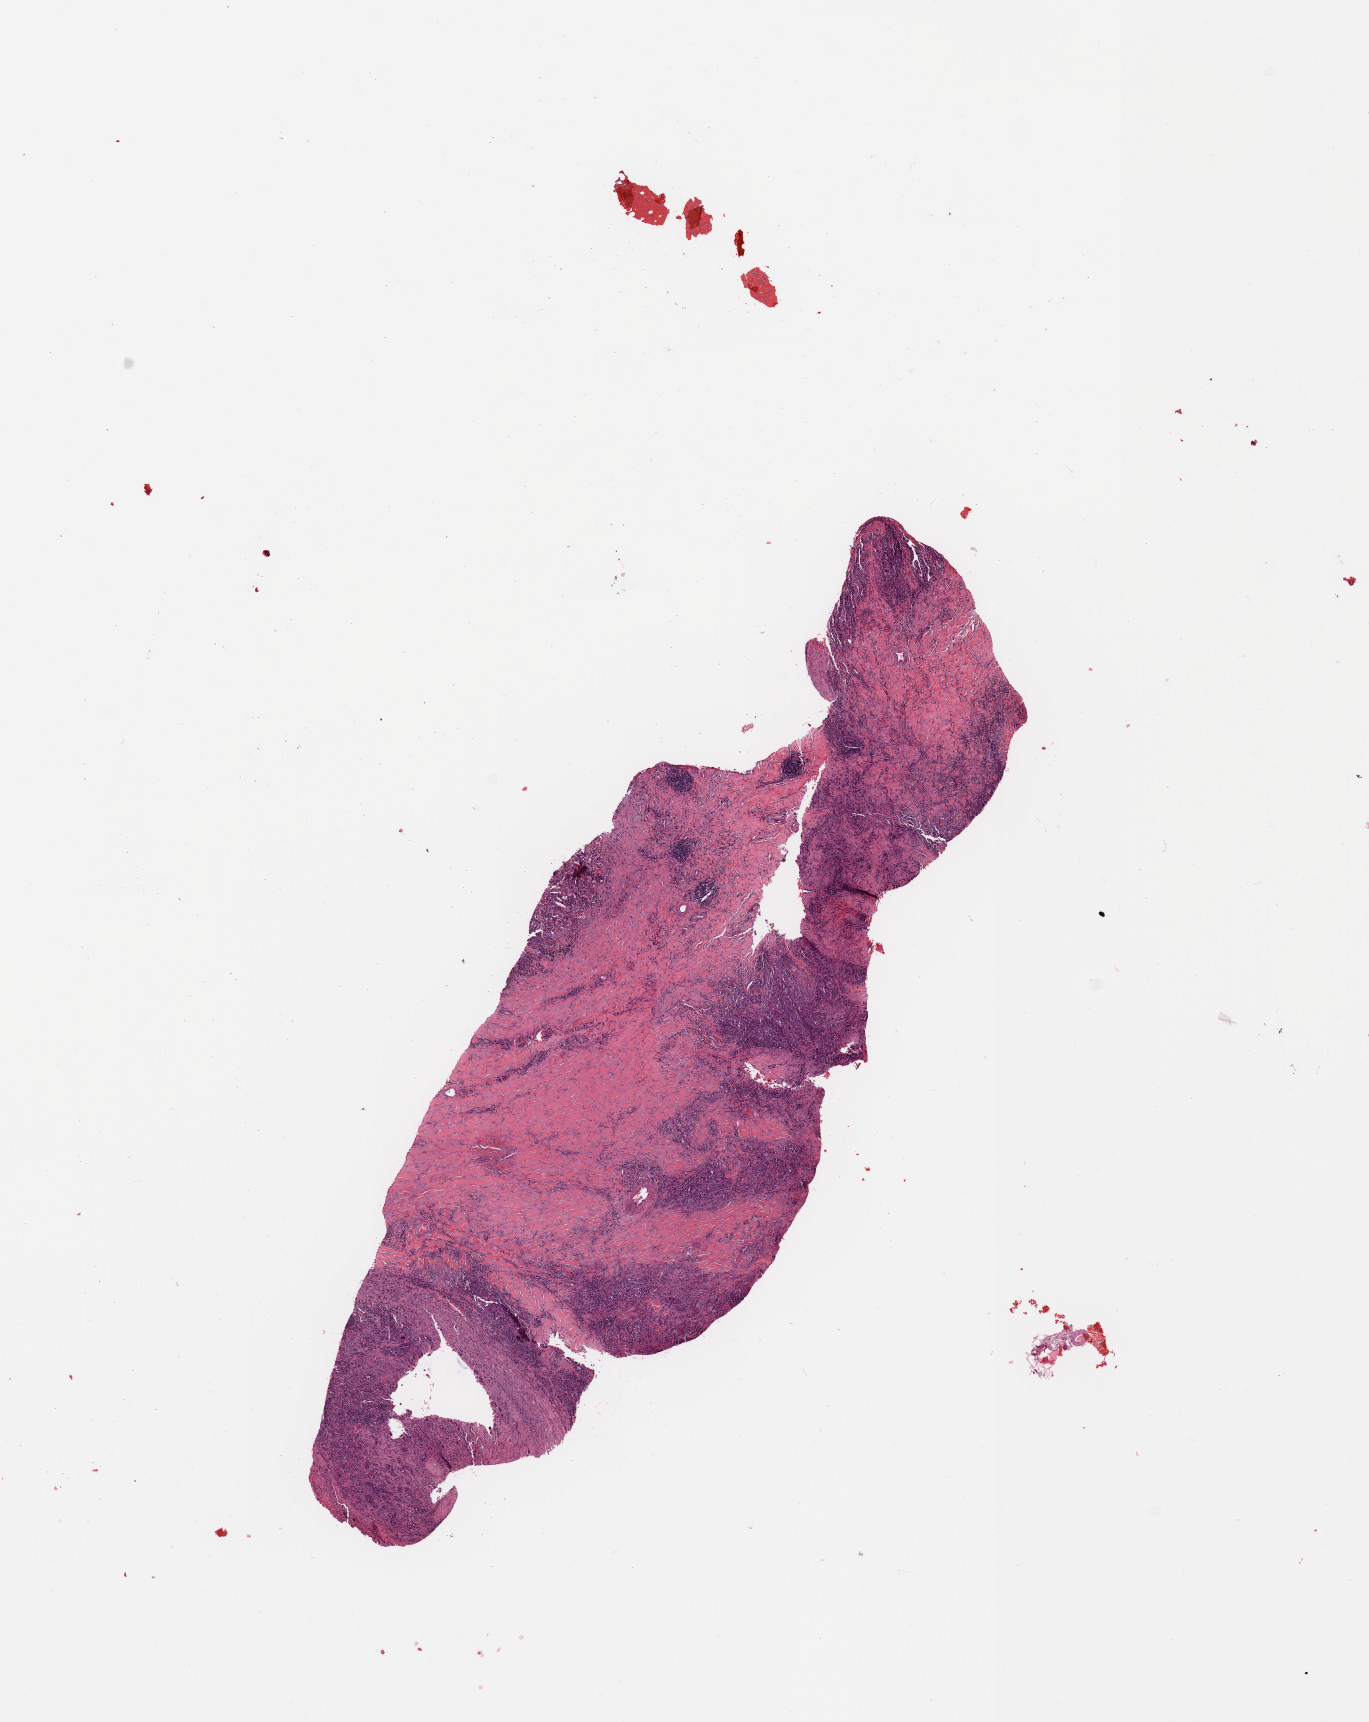
Whole-slide histology image, H&E-stained, whole scanned area (about 10.8 x 13.6 mm, slide scanned at 20x) shown as a low-resolution overview, lung, tumour tissue. 88-year-old male patient.
Diagnosis: Squamous cell carcinoma, NOS.